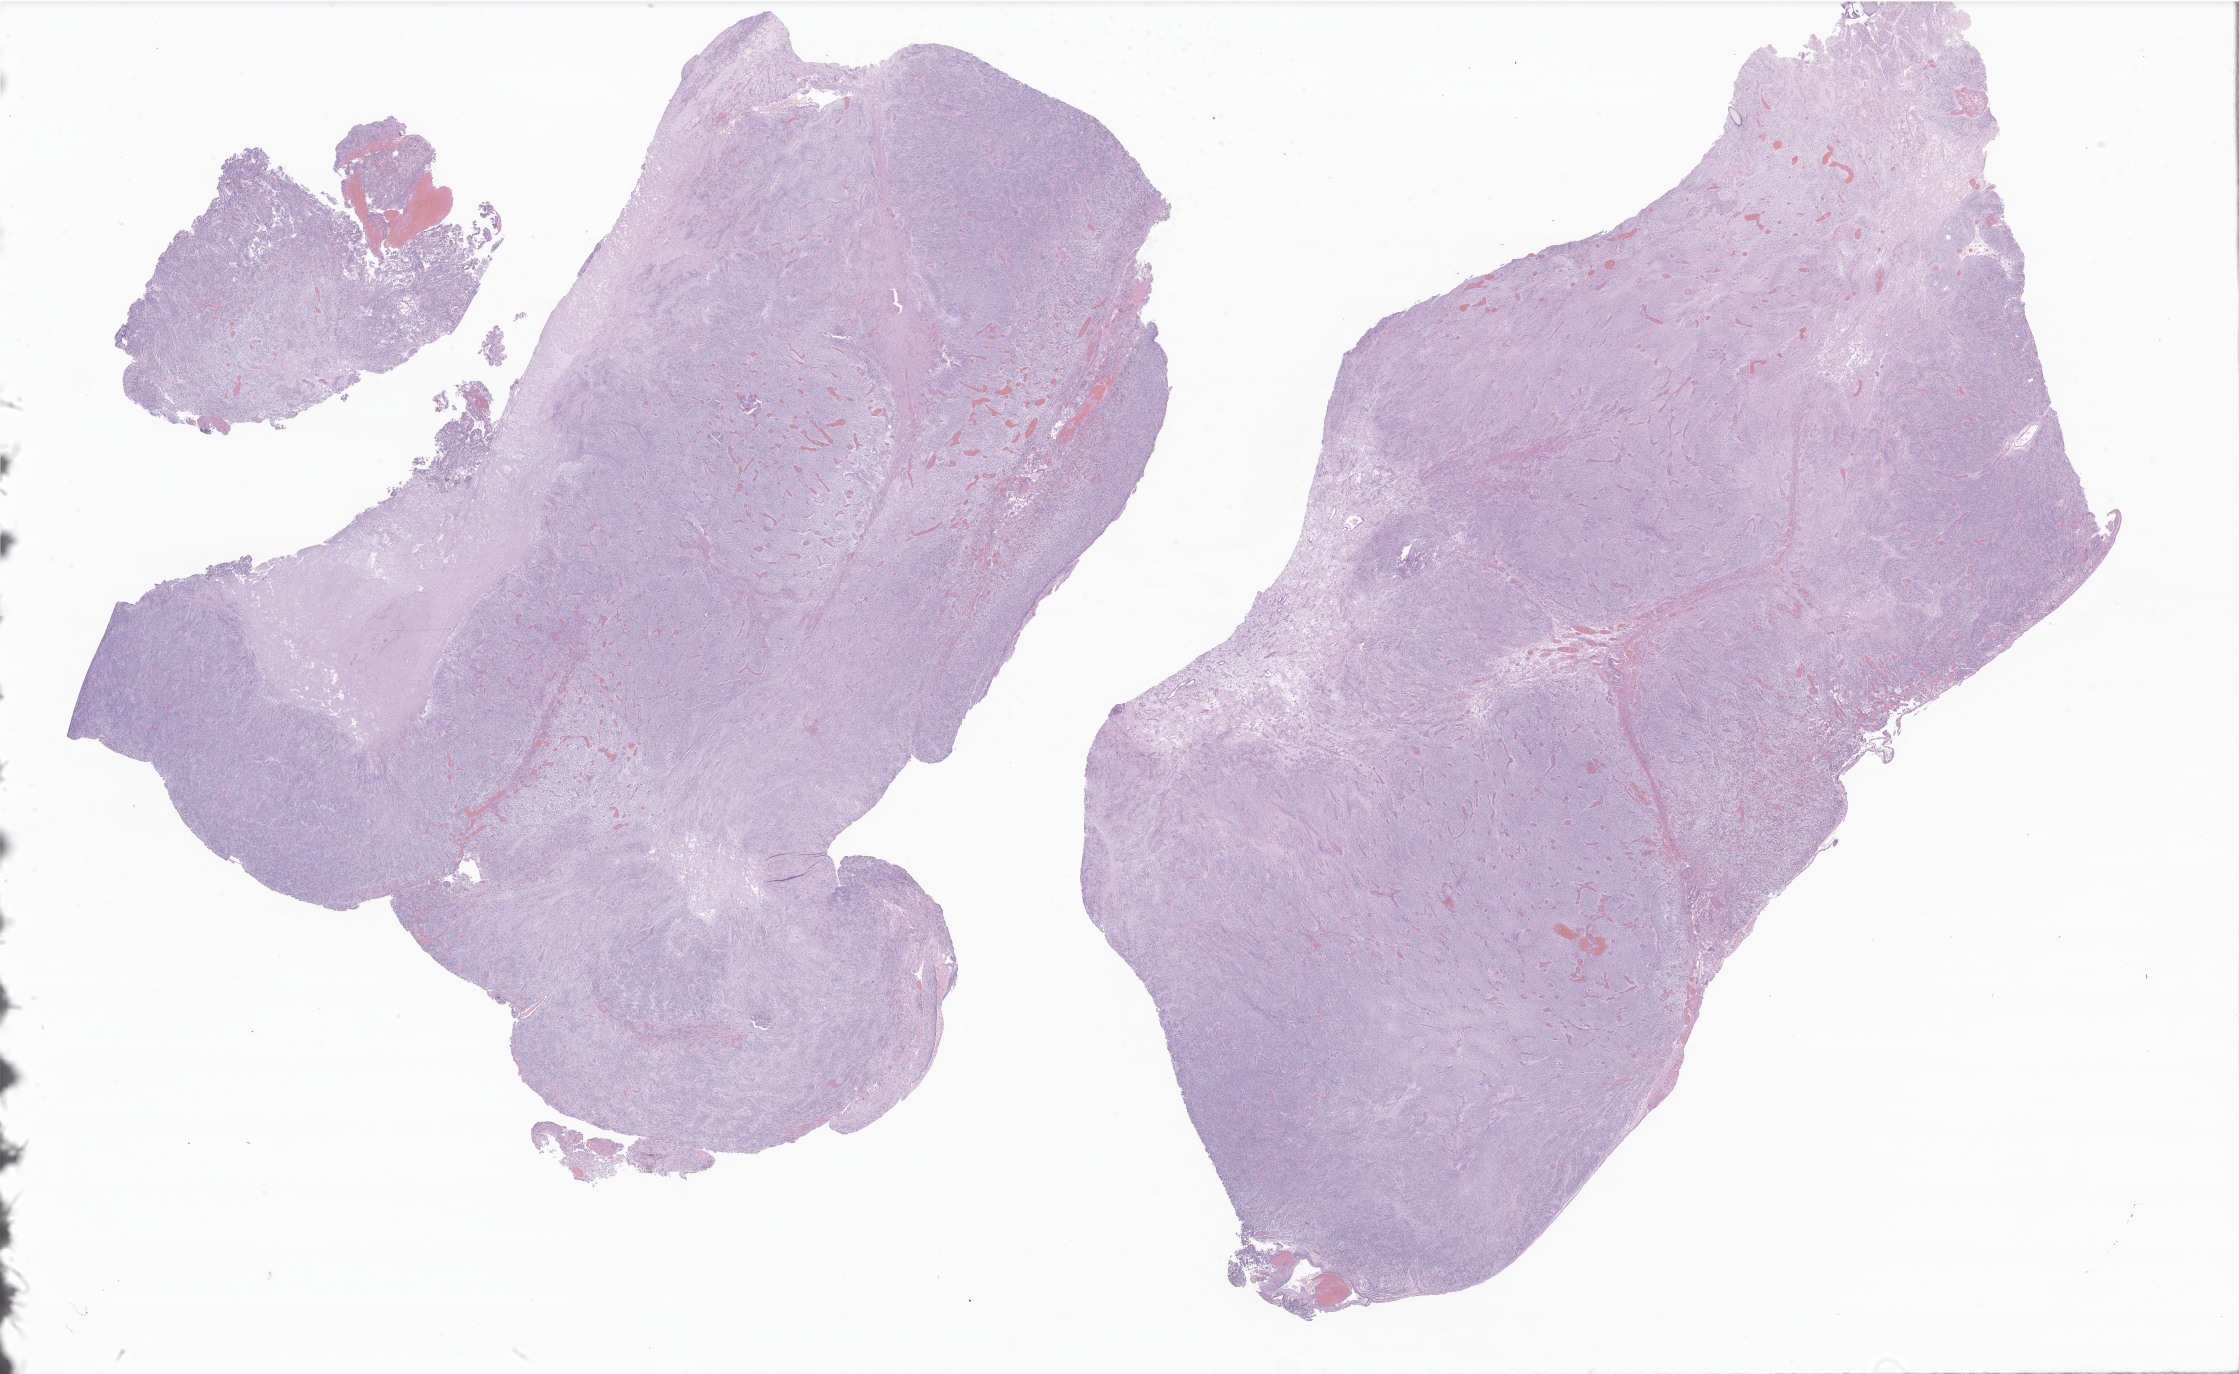
Whole-slide image, hematoxylin and eosin (H&E) stain of tumor tissue from the frontal lobe, whole scanned area (about 37.8 x 23.2 mm) shown as a low-resolution overview. FFPE section. Female patient, age 153 months (12 years 9 months).
Diagnosis: Neoplasm, uncertain whether benign or malignant.